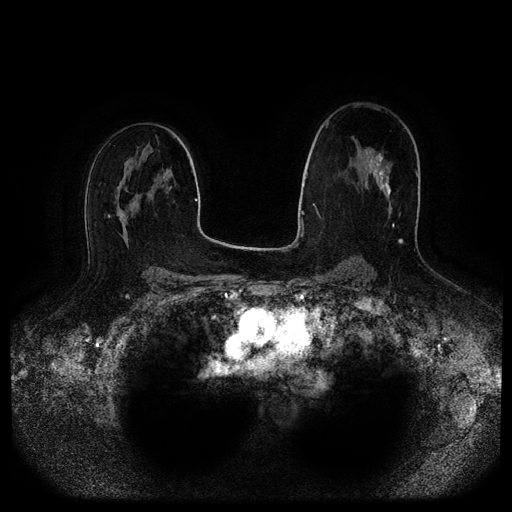
Breast MRI (dynamic contrast-enhanced, multi-phase), one axial slice; slice 59 of 116 in the series (ordered by position); dynamic contrast-enhanced series, time point 2 of 5 at this slice position (early post-contrast); 1.5 T; TE 2.6 ms, TR 5.2 ms; 2 mm slice thickness; 512 × 512 image matrix. Patient: female, 45 years.
Annotated regions visible in this slice (semi-automatic segmentation, software-assisted and operator-edited):
- breast lesion (labelled benign in the annotation): bounding box (x1, y1, x2, y2) in pixels: (364, 181, 368, 187)